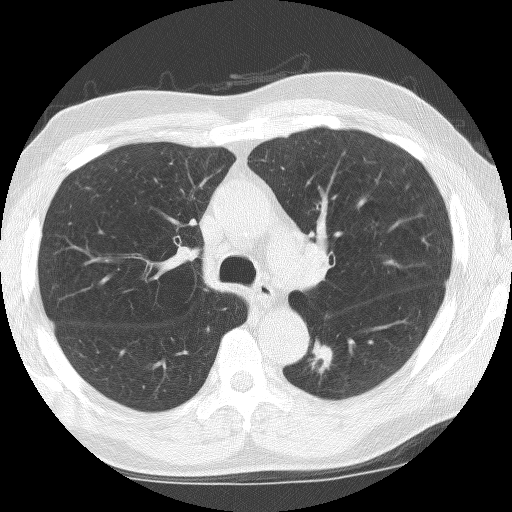
Axial slice from a low-dose chest CT screening exam. First (baseline) screen. Lung window (W 1500 / L -600 HU). 2.5 mm slice thickness. Lung (sharp) reconstruction kernel (BONE). Male, age 67 years at enrolment.
• Lesion marked by an expert reader, bounding box [x1, y1, x2, y2] px = [296, 337, 342, 388].
• Screening reader's record for this exam (one nodule recorded; not confirmed to be the boxed lesion): non-calcified nodule or mass ≥4 mm, left lower lobe, 18 × 13 mm, spiculated (stellate) margins, soft tissue attenuation.
• Official screen result: positive, change unspecified: nodule(s) >= 4 mm or enlarging nodule(s), mass(es), or other non-specific abnormalities suspicious for lung cancer.
• Lung cancer was diagnosed 5 days after this screen: non-small cell carcinoma, left lower lobe, undifferentiated (G4), stage IA (AJCC 6th edition), 12 mm at pathology.